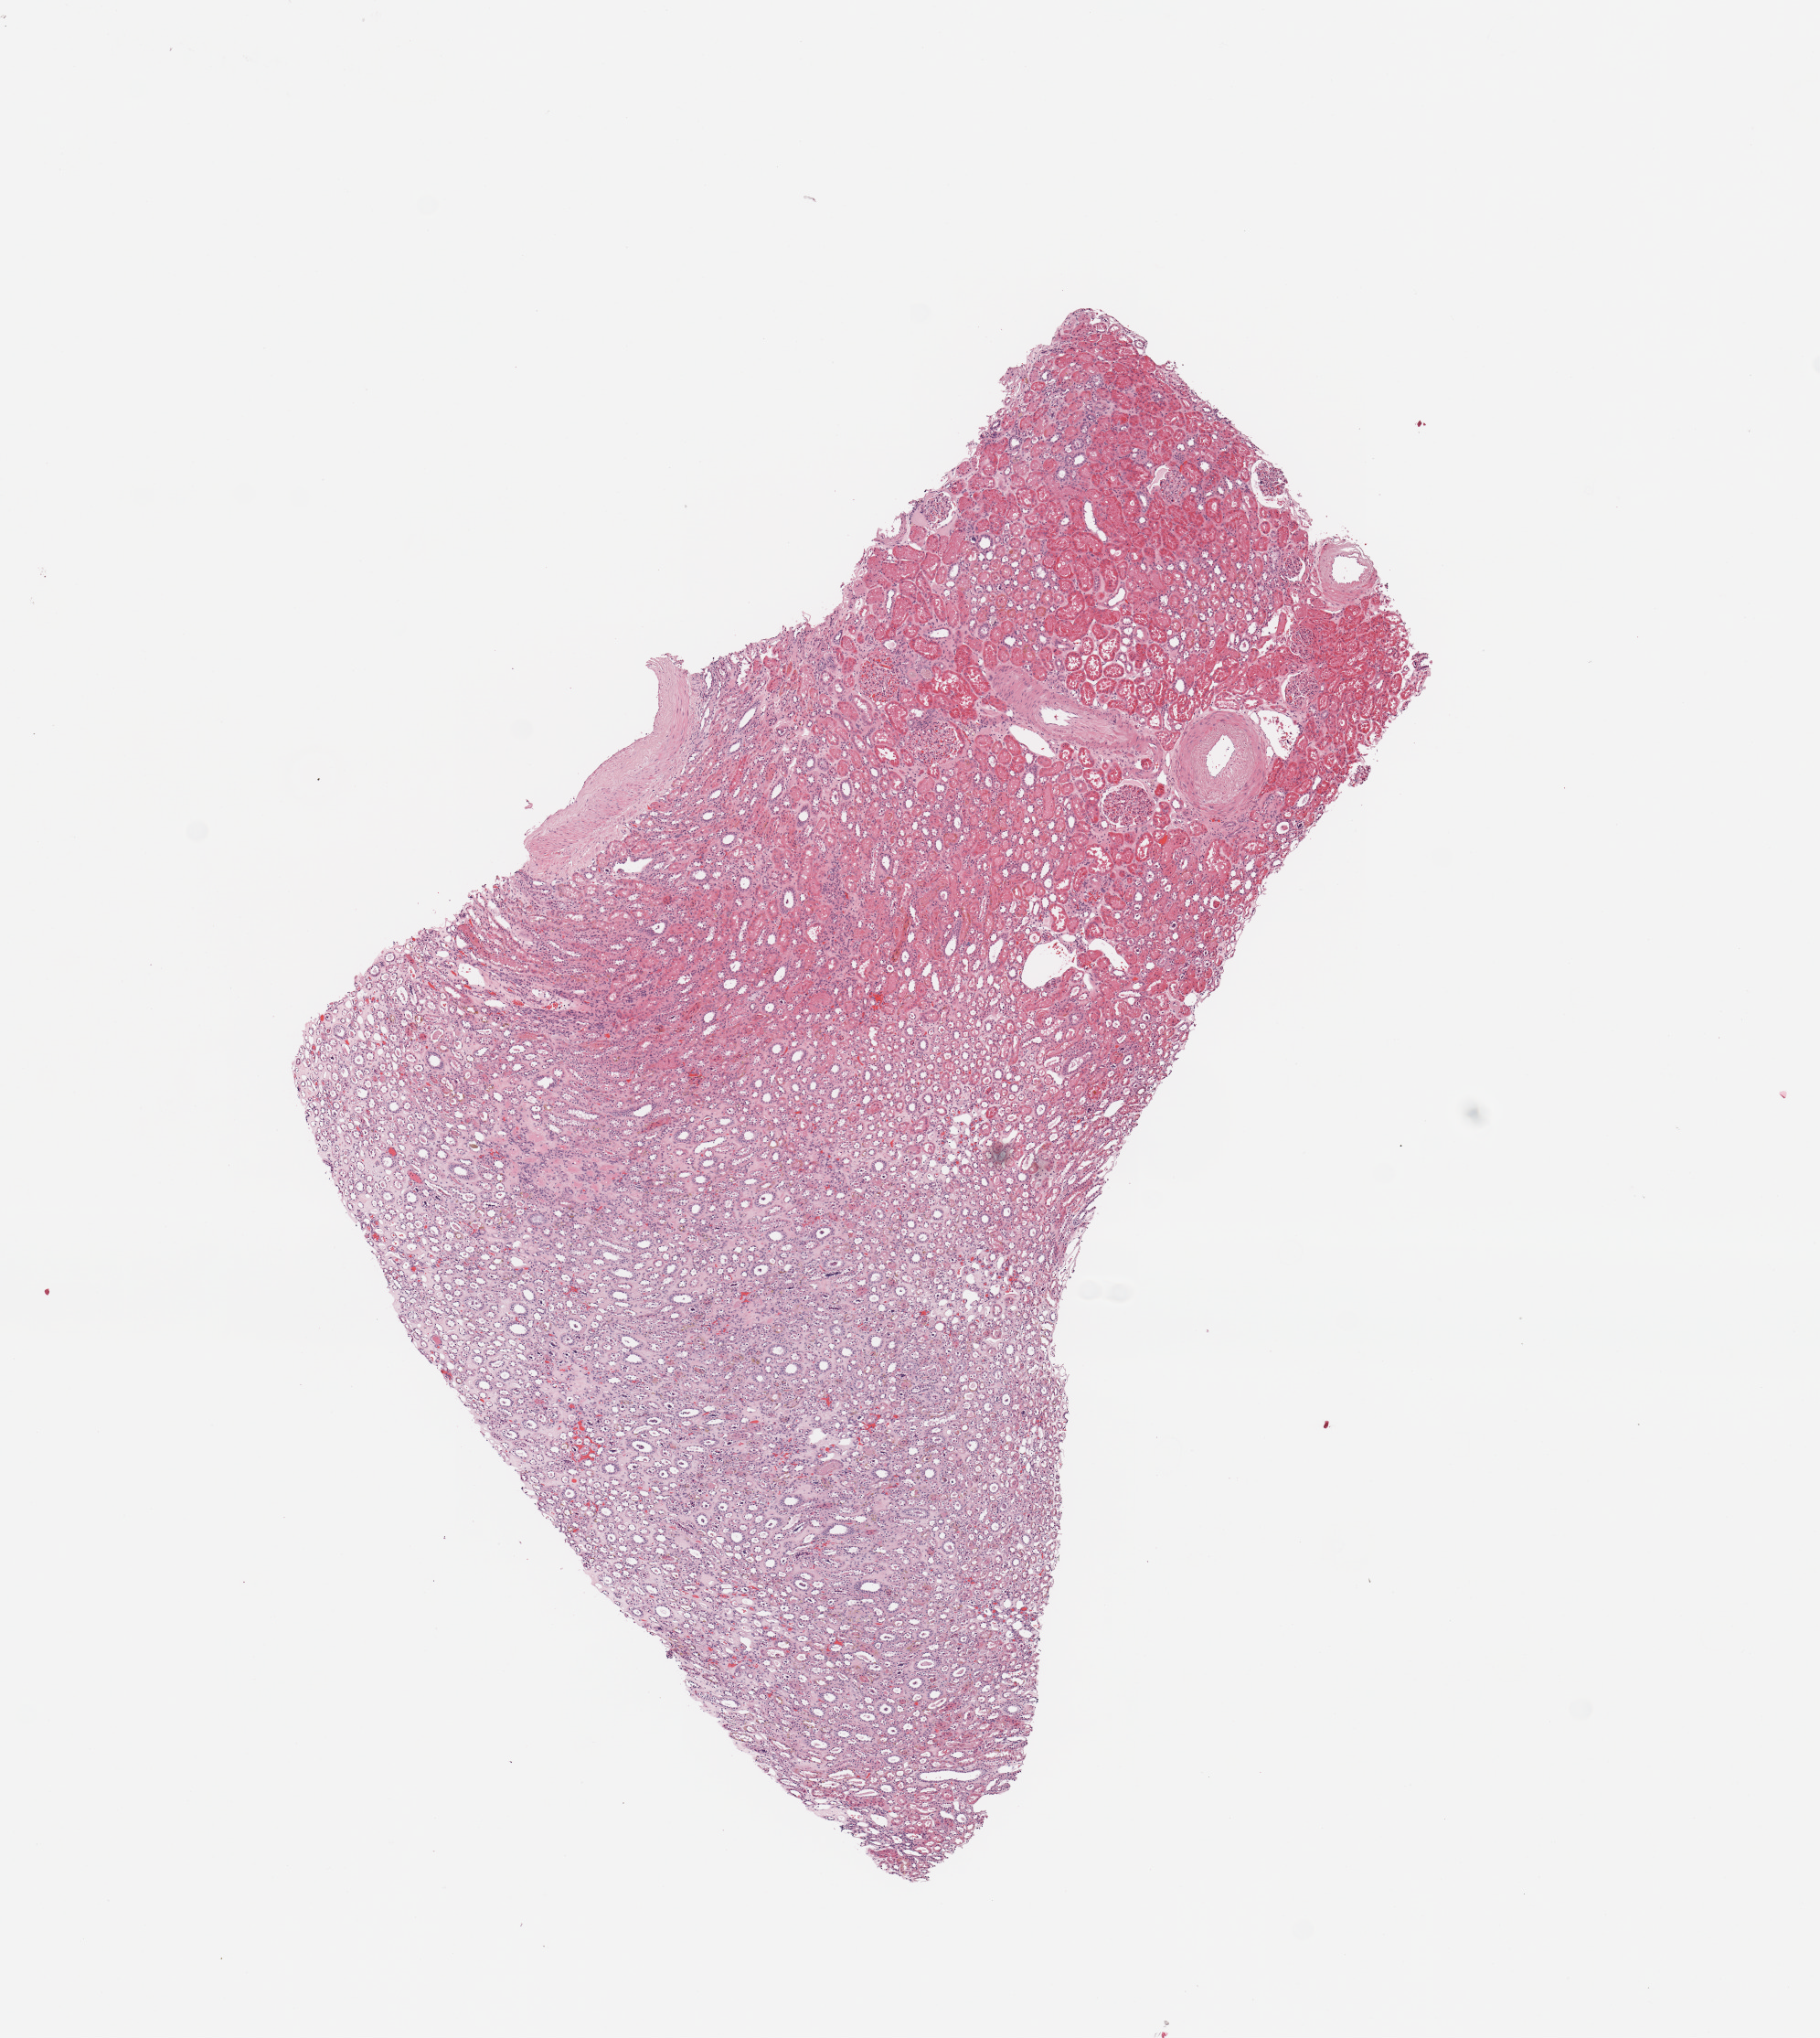
Whole-slide histology image, H&E-stained — whole scanned area (about 7.9 x 8.8 mm, from a 20x scan) shown as a low-resolution overview. Kidney, normal (non-tumour) tissue. Patient: male, age 76 years.
This section: normal (non-tumour) tissue from the same patient. Patient diagnosis: Renal cell carcinoma, NOS.